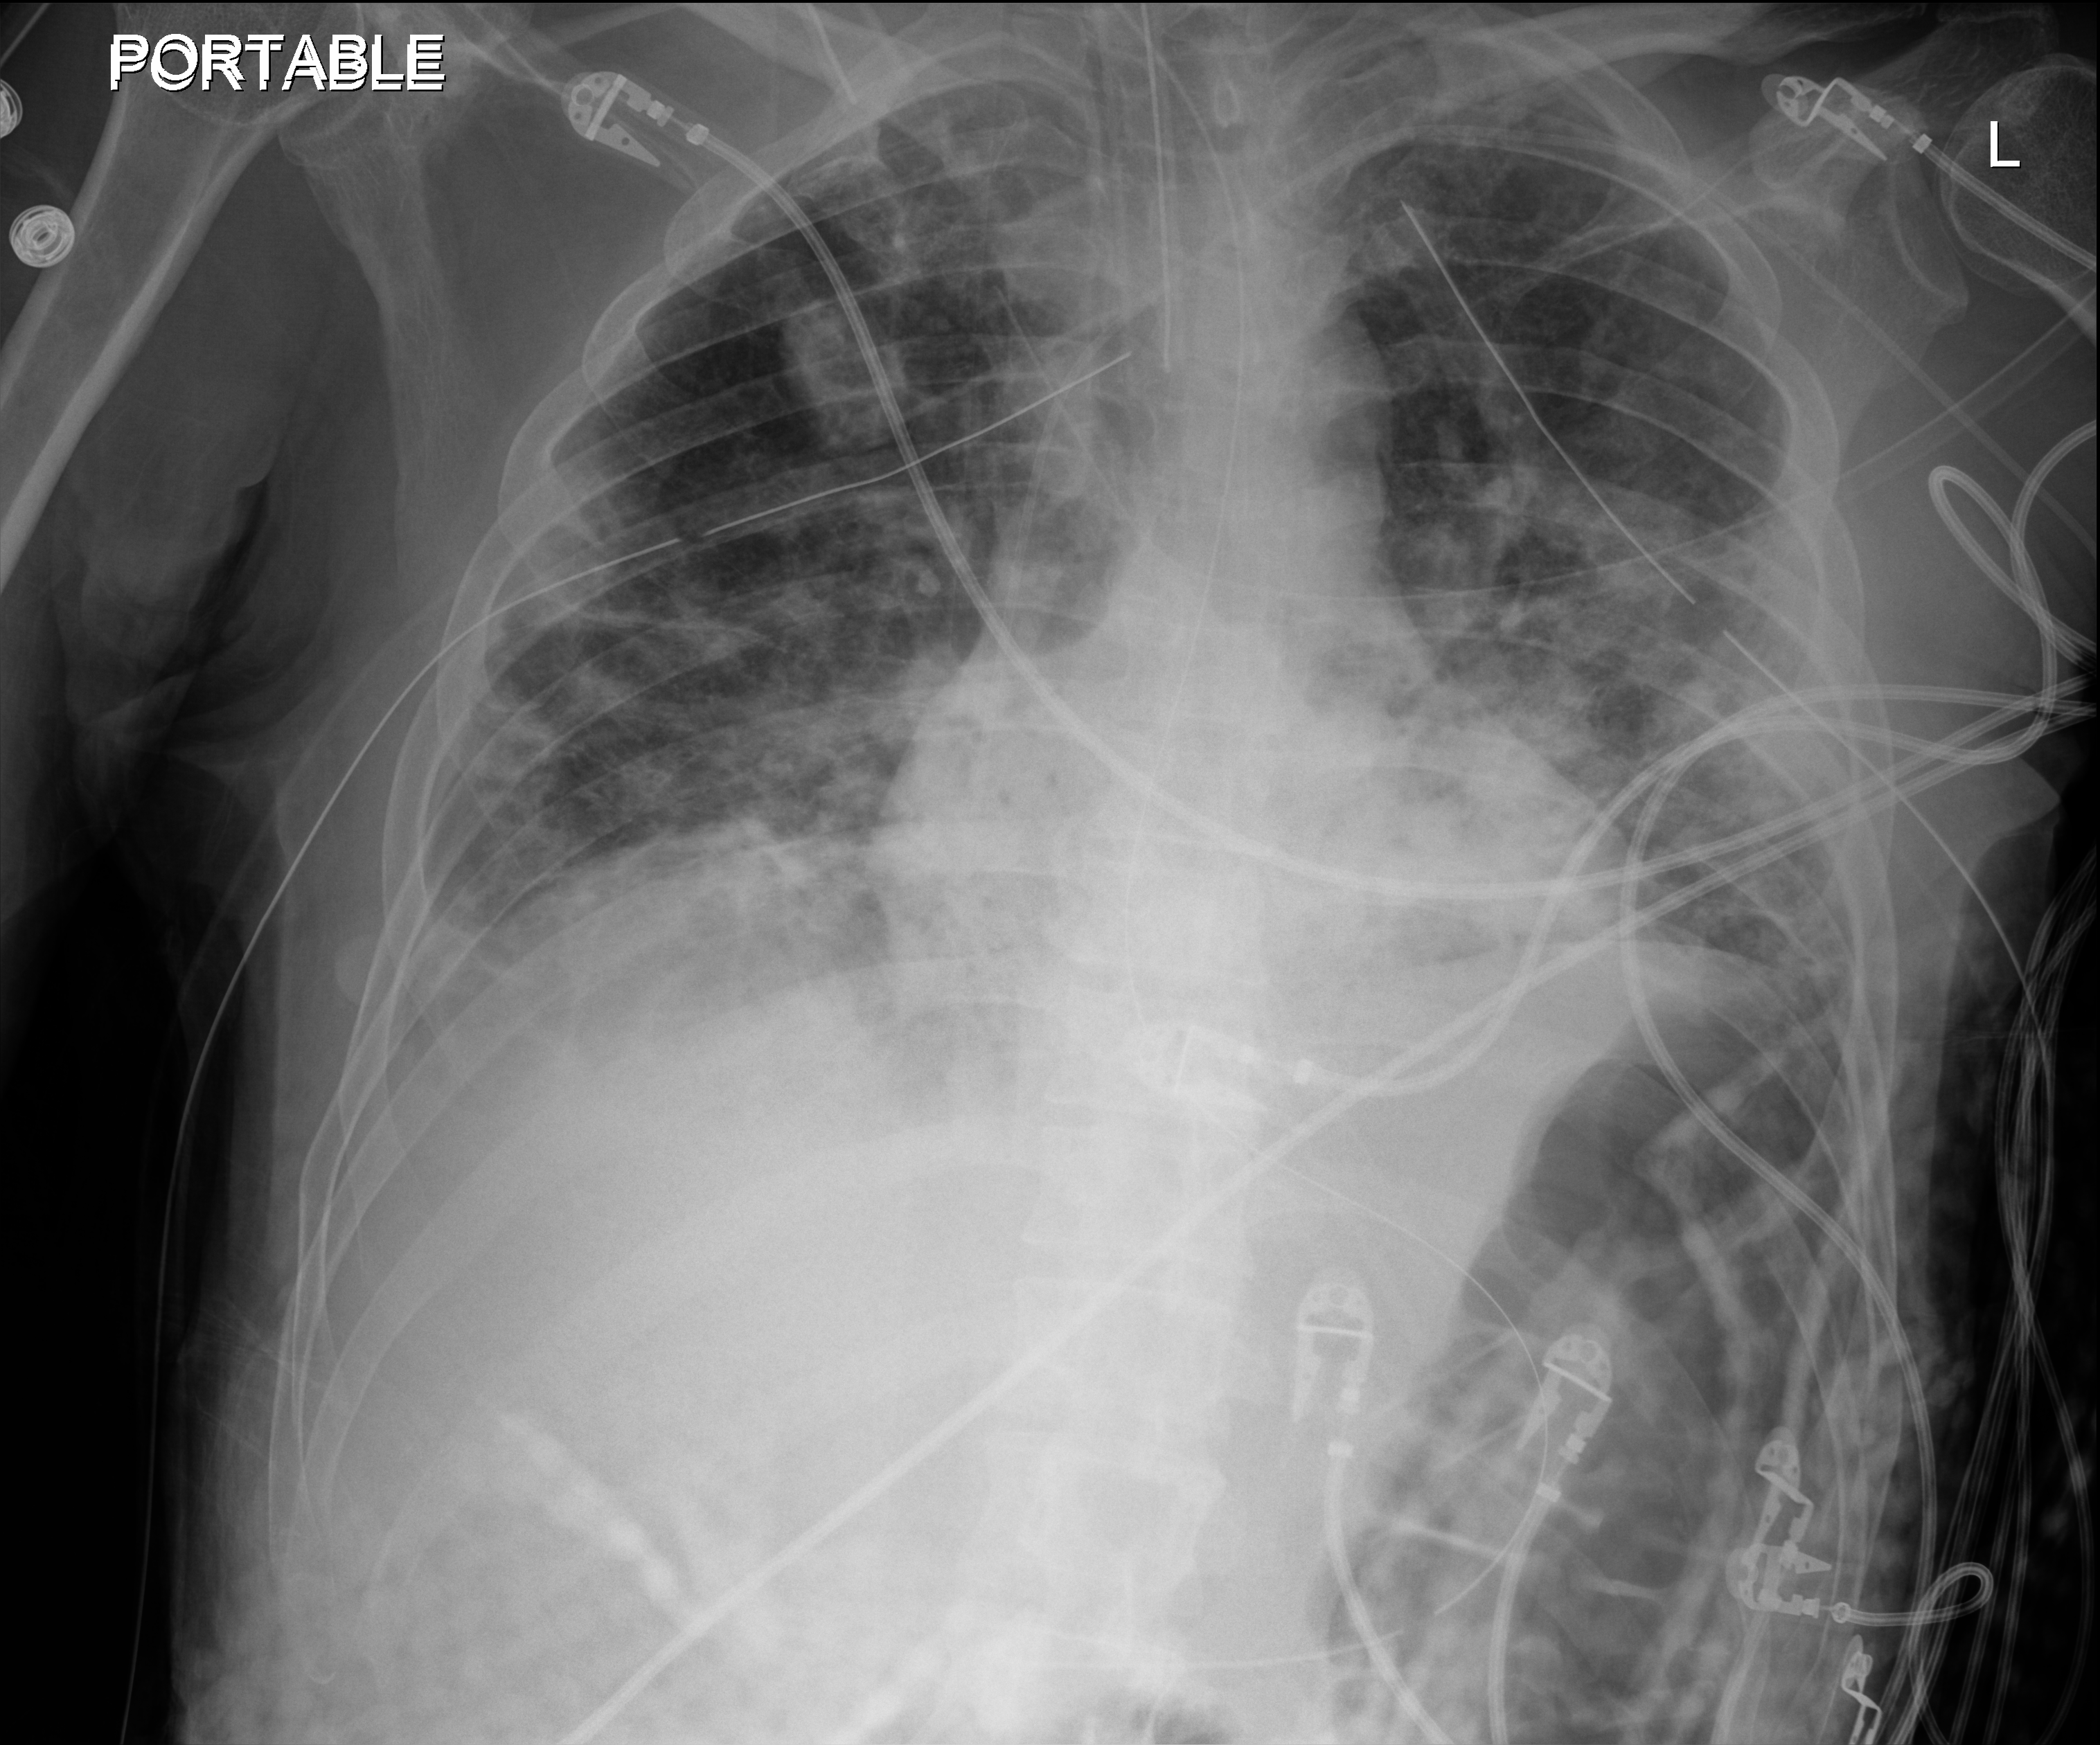
Portable chest radiograph; anteroposterior (AP) projection. Male patient hospitalised with COVID-19, age 18–59 years.
Hospital-stay facts (about this admission, not read from this image; timing relative to this image not recorded):
- mechanically ventilated during this hospital stay: yes
- other chronic lung disease (admission record): no